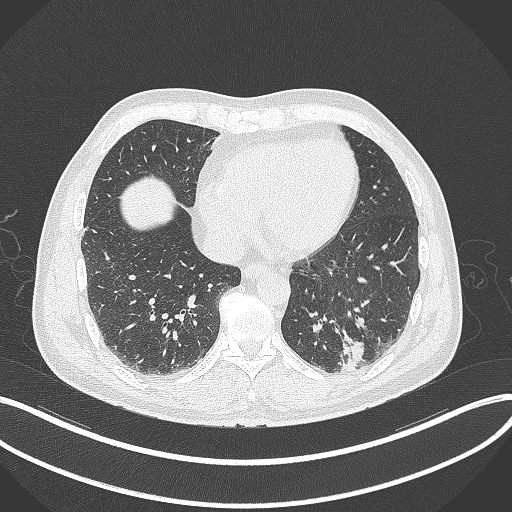
Chest CT, one axial slice. 120 kVp. Lung window (W 1500 / L -600 HU). 1 mm slice thickness. 512 × 512 image matrix. Male patient, age 54 years. From the clinical record (not read from this slice): clinical TNM (as recorded): T1c N0 M1; histopathological grade: G3.
Annotated regions visible in this slice (bounding box drawn by a radiologist):
- lung tumour (recorded histology: adenocarcinoma): bounding box (x1, y1, x2, y2) in pixels: (336, 333, 368, 375)